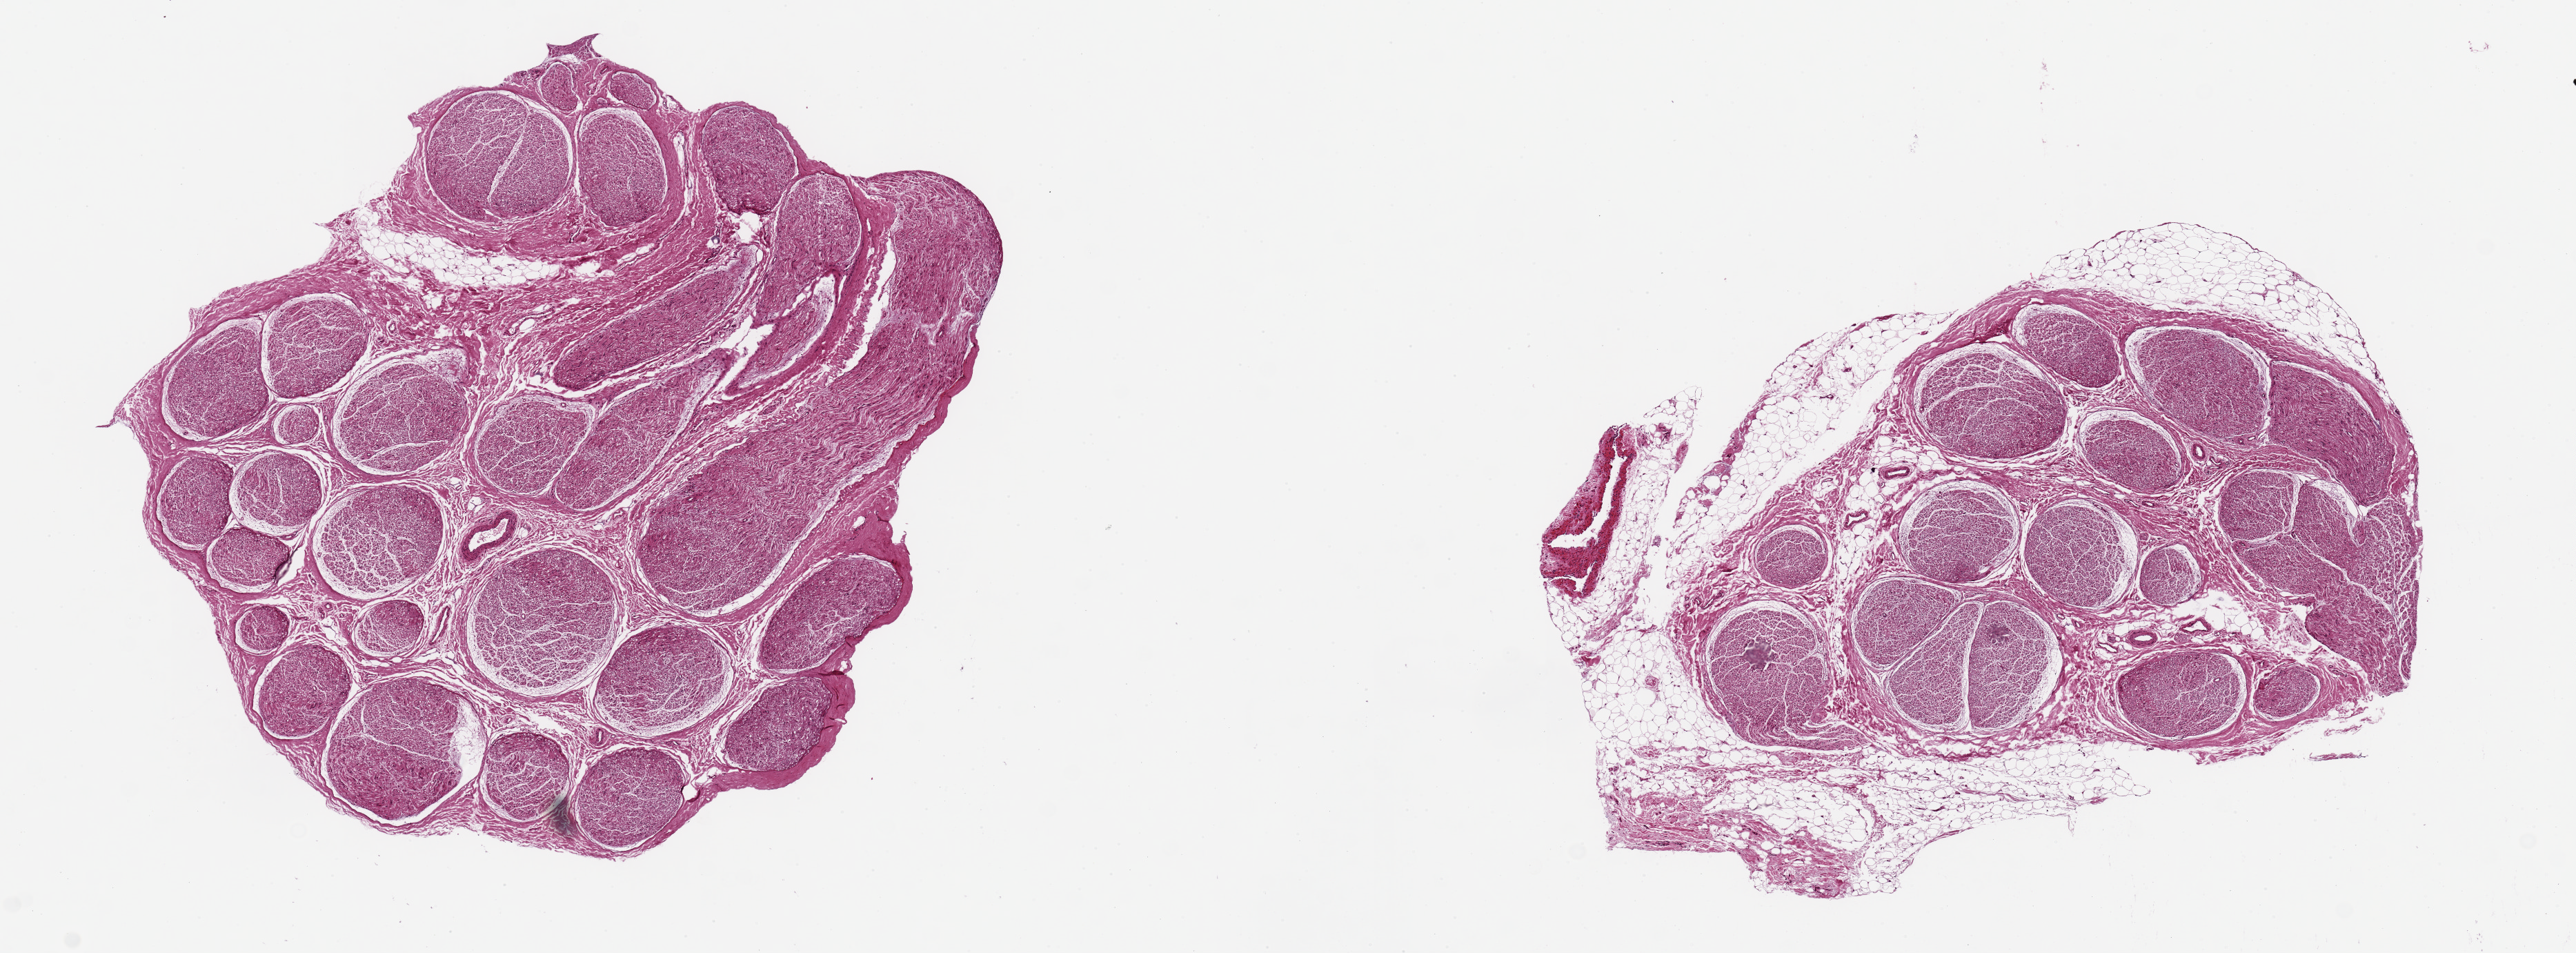
Digitized haematoxylin and eosin-stained section — low-resolution overview of the scanned area, about 14.8 x 5.5 mm (from a 20x scan). PAXgene-fixed paraffin-embedded (PFPE) section. Target tissue: tibial nerve. Donor tissue sample. Donor: female.
Pathologist's review note for this sample: 2 pieces ~5mm in diameter; one with 30% surrounding adipose, other 'clean'.